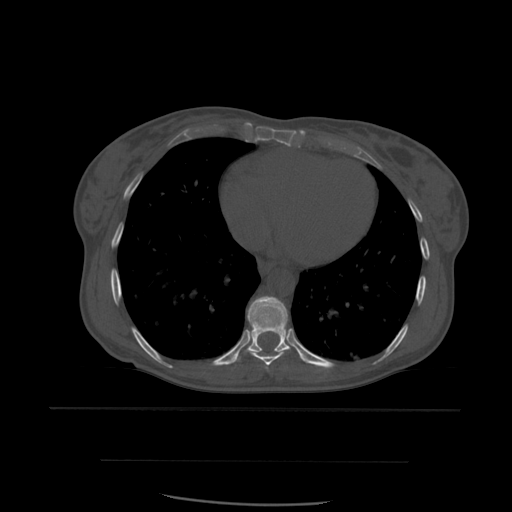
CT including the spine, one axial slice; position 346 of 574 along the scan axis; bone window (W 1800 / L 400 HU); 512 × 512 image matrix, field of view 392 × 392 mm. Patient age 48 years. From the clinical record (not read from this slice): primary cancer: lung.
Annotated regions visible in this slice (semi-automatically segmented with operator editing):
- T8 vertebra: box from (x=245, y=349) to (x=285, y=371) px
- T9 vertebra: (x=233, y=296)–(x=313, y=365)